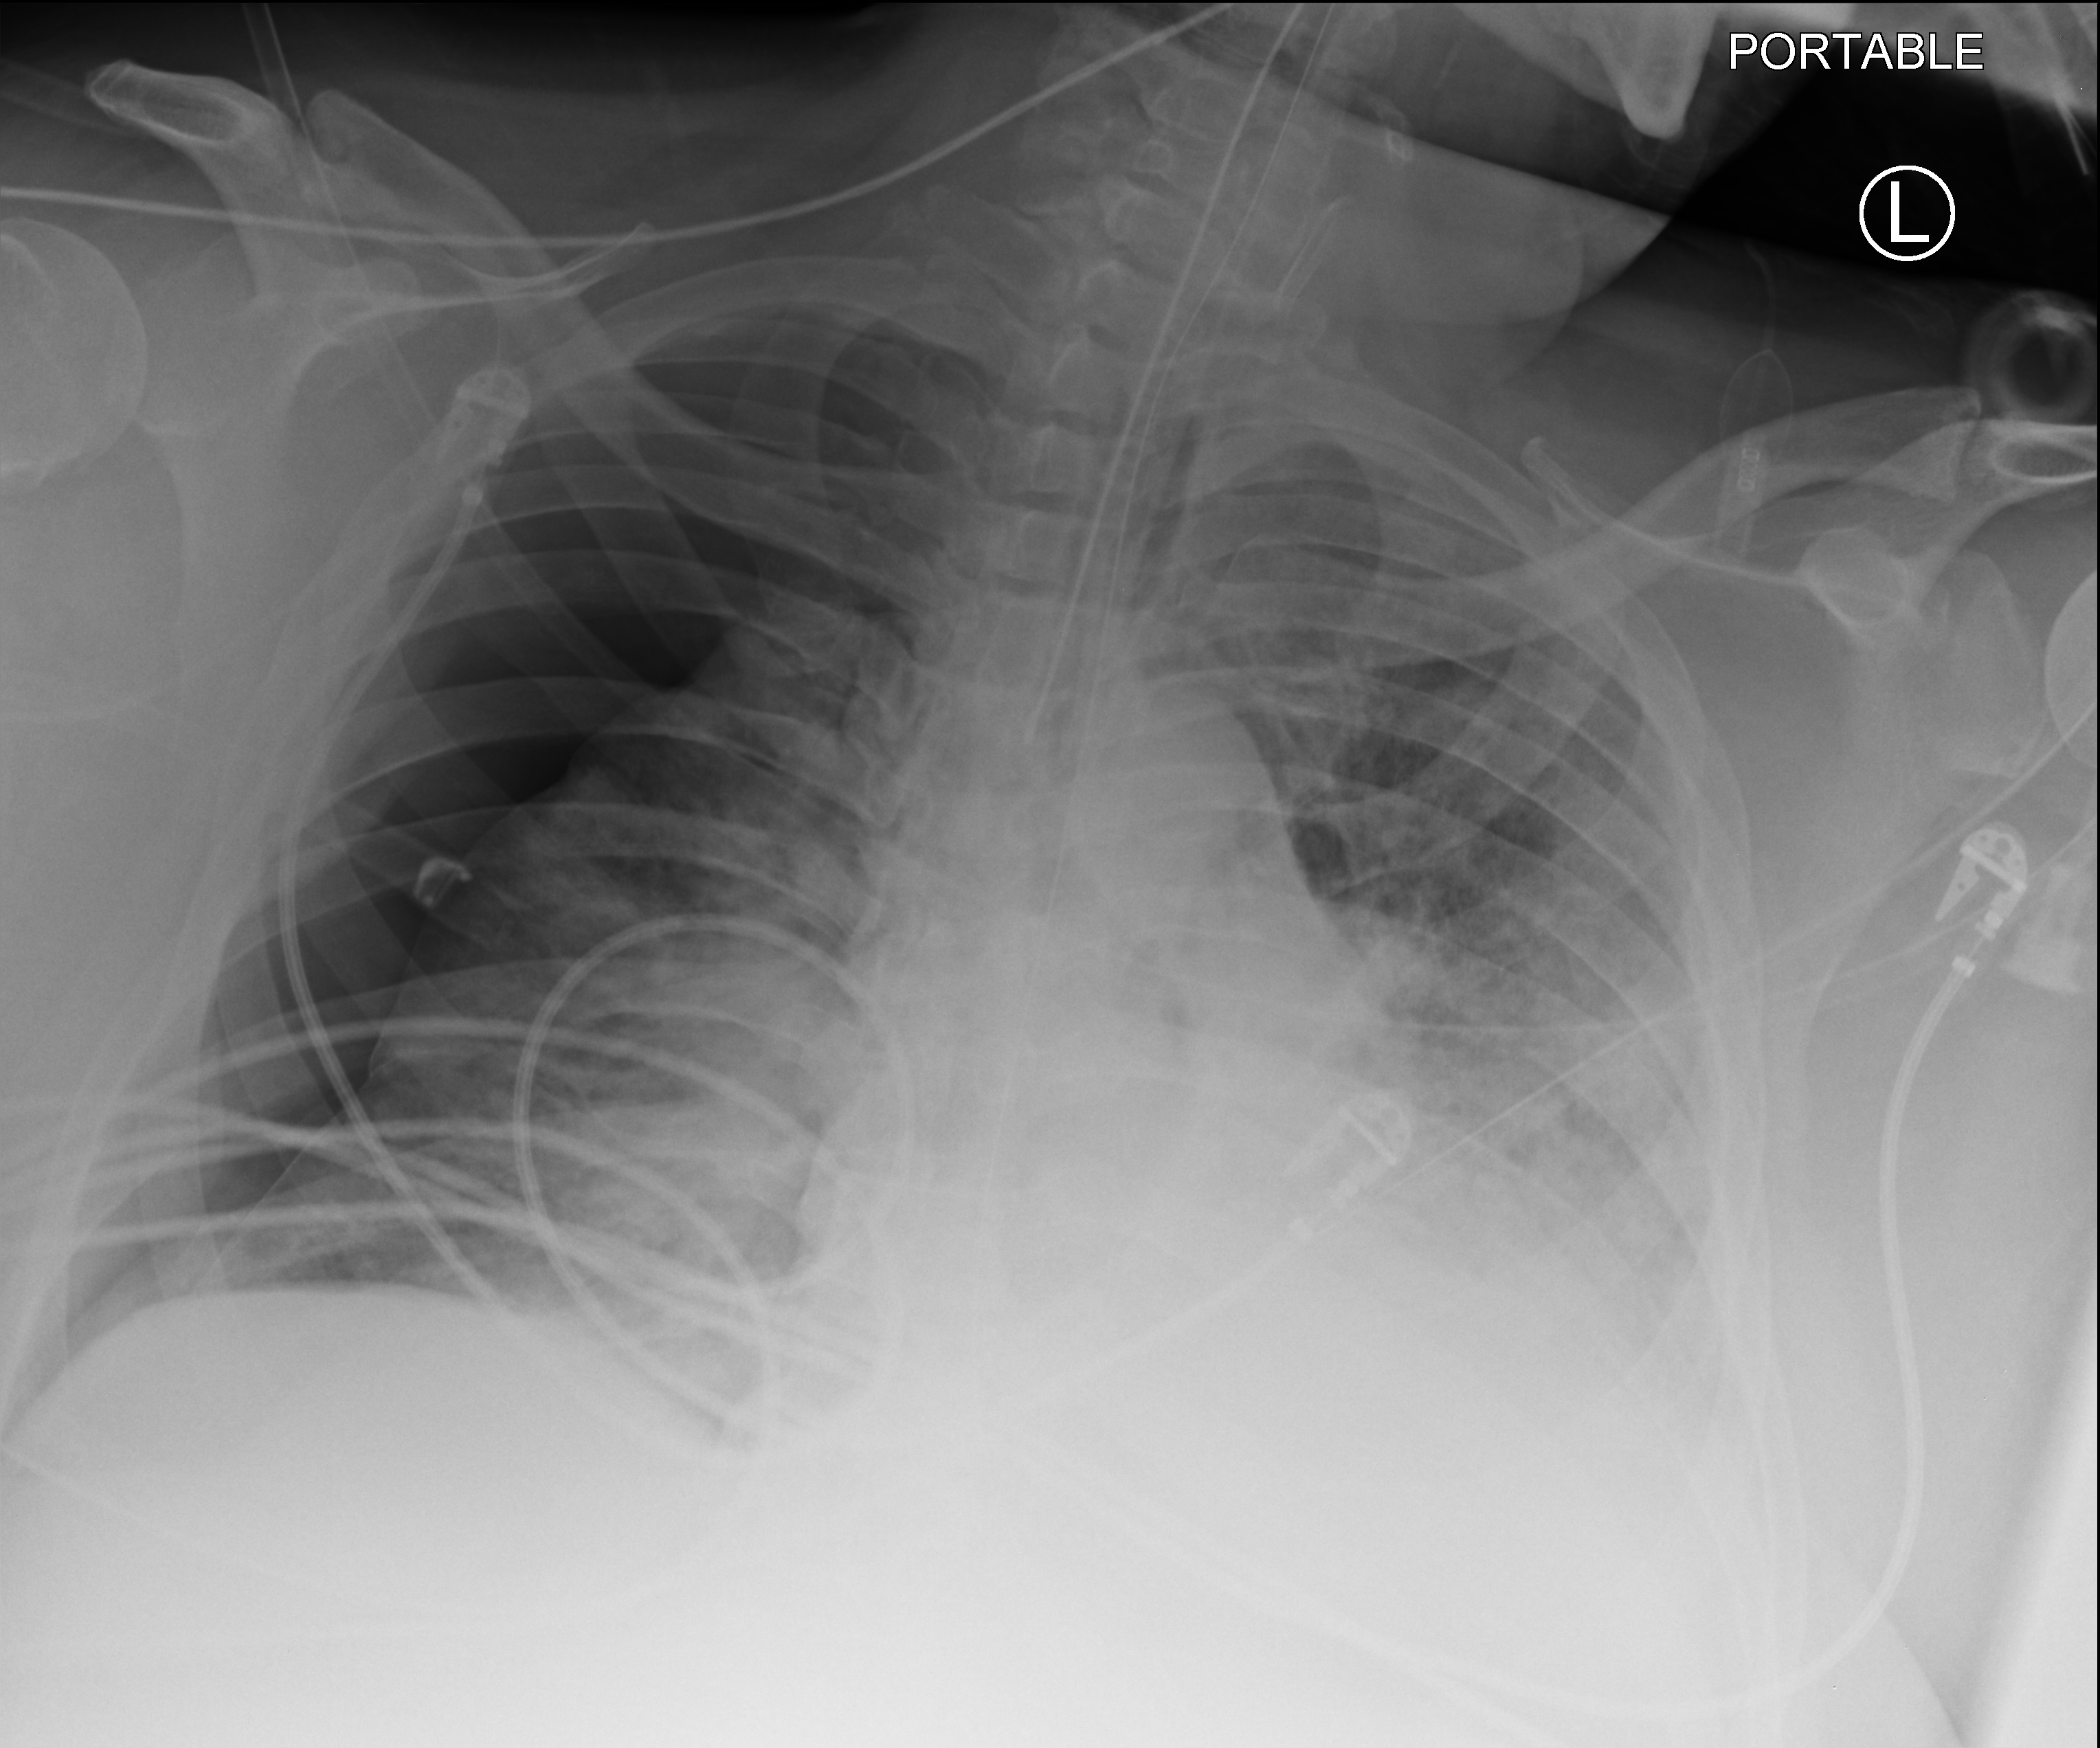
Portable chest radiograph, anteroposterior (AP) projection. Patient hospitalised with COVID-19; male, aged 60–74 years.
Admission-level facts for this patient (not findings on this image; timing relative to this image not recorded): length of hospital stay: 34 days; admitted to intensive care during this hospital stay: yes.